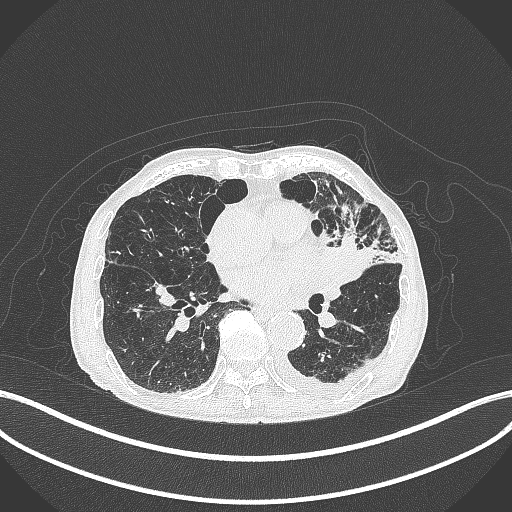
Chest CT, one axial slice; reconstruction kernel B70f; lung window (W 1500 / L -600 HU); 1 mm slice thickness; 512 × 512 image matrix, field of view 400 × 400 mm. Patient: male, 90 years or older. From the clinical record (not read from this slice): clinical TNM (as recorded): T2b N1 M0.
Annotated regions visible in this slice (rectangle marked by the reading radiologist):
- lung tumour (recorded histology: squamous cell carcinoma): bounding box (x1, y1, x2, y2) in pixels: (326, 246, 372, 285)